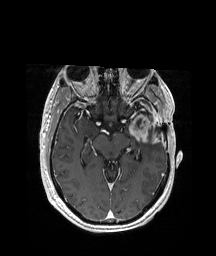
Brain MRI from a brain-tumour surgery series, one axial slice. Position 120 of 208 along the scan axis. T1-weighted post-contrast. 1 mm slice thickness. 216 × 256 image matrix, field of view 228 × 270 mm. Case-level facts recorded for this patient, not image findings: histopathology: Glioblastoma; WHO grade: 4; IDH mutation: no.
Structures marked on this image (expert manual segmentation):
- previous resection cavity: bounding box <136,119,160,132> (left, top, right, bottom; pixels)
- tumour: <123,112,158,140>